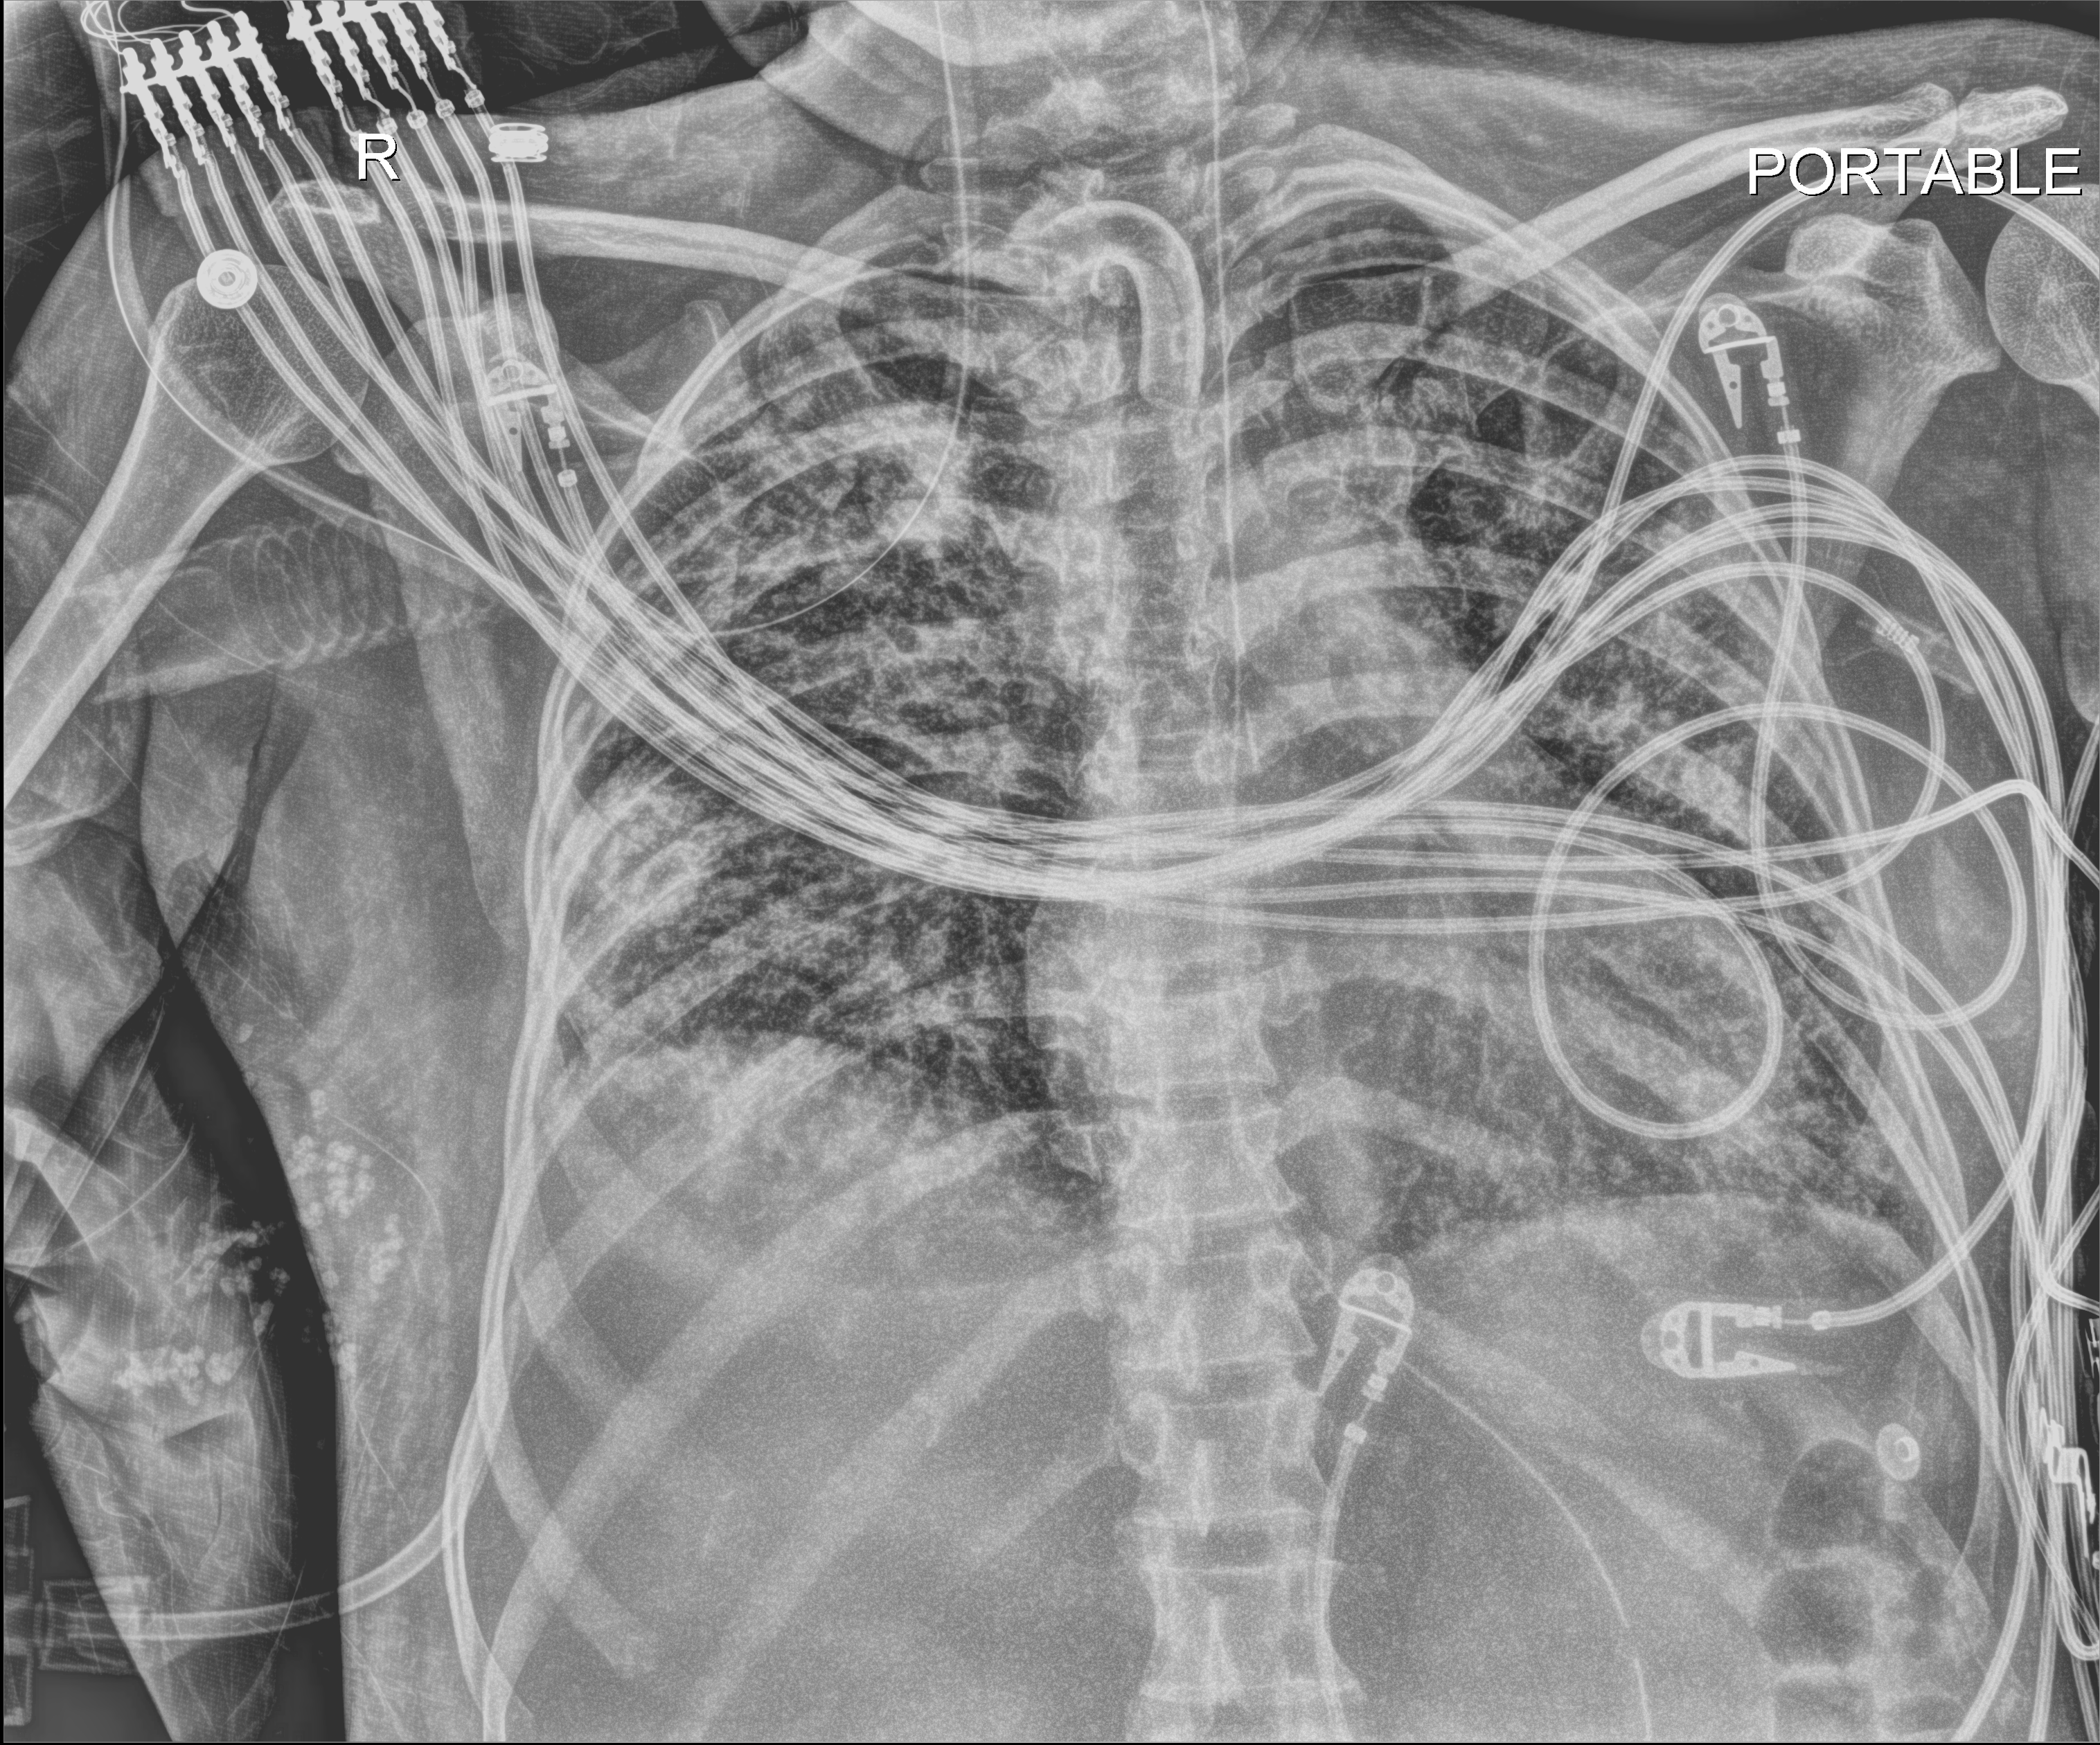
Portable chest radiograph, anteroposterior (AP) projection. Female patient hospitalised with COVID-19, age 18–59 years.
Admission-level facts for this patient (not findings on this image; timing relative to this image not recorded):
- smoking status (admission record): former
- diabetes (admission record): no
- admitted to intensive care during this hospital stay: yes